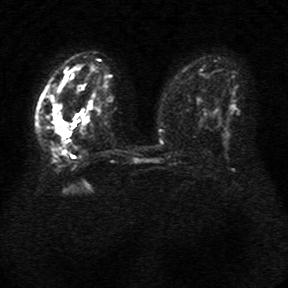
Breast MRI, one axial slice. Position 17 of 34 along the scan axis. Diffusion-weighted series; image 2 of 4 stored at this slice position (different b-values; order by instance number). 1.5 T. 288 × 288 image matrix, field of view 340 × 340 mm. Female patient.
Annotated regions visible in this slice (expert manual segmentation):
- tumour on diffusion-weighted imaging: bounding box [x1, y1, x2, y2] px = [53, 100, 68, 137]